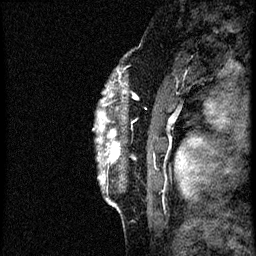
Breast MRI (dynamic contrast-enhanced), one sagittal slice; position 7 of 56 along the scan axis; dynamic contrast-enhanced study with each time point stored as its own series, time point 2 of 3 at this slice position (early post-contrast, ordered by acquisition time); 1.5 T; TE 4.2 ms, TR 21.3 ms; 2 mm slice thickness; 256 × 256 image matrix, field of view 200 × 200 mm. Female patient, age 41 years. Case-level facts recorded for this patient, not image findings: setting: breast cancer imaged before/during neoadjuvant chemotherapy; receptor status: HER2-positive.
Structures marked on this image (semi-automatically segmented with operator editing):
- analysis volume of interest (the breast-tissue region the enhancement analysis was run in; not a lesion): bounding box [x1, y1, x2, y2] px = [94, 73, 177, 205]
- tumour enhancement mask (voxels above the 100 % enhancement threshold inside the analysis volume of interest): [111, 130, 119, 158]